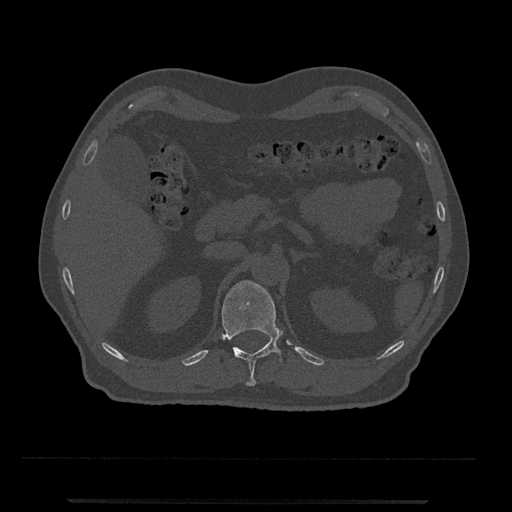
CT including the spine, one axial slice. Slice 395 of 797 in the series (ordered by position). Reconstruction kernel Br40s/3. 120 kVp. Bone window (W 1800 / L 400 HU). 512 × 512 image matrix. Male patient, age 63 years. Case-level facts recorded for this patient, not image findings: primary cancer: prostate.
Annotated regions visible in this slice (semi-automatic segmentation, software-assisted and operator-edited):
- T12 vertebra: box from (x=222, y=280) to (x=282, y=386) px